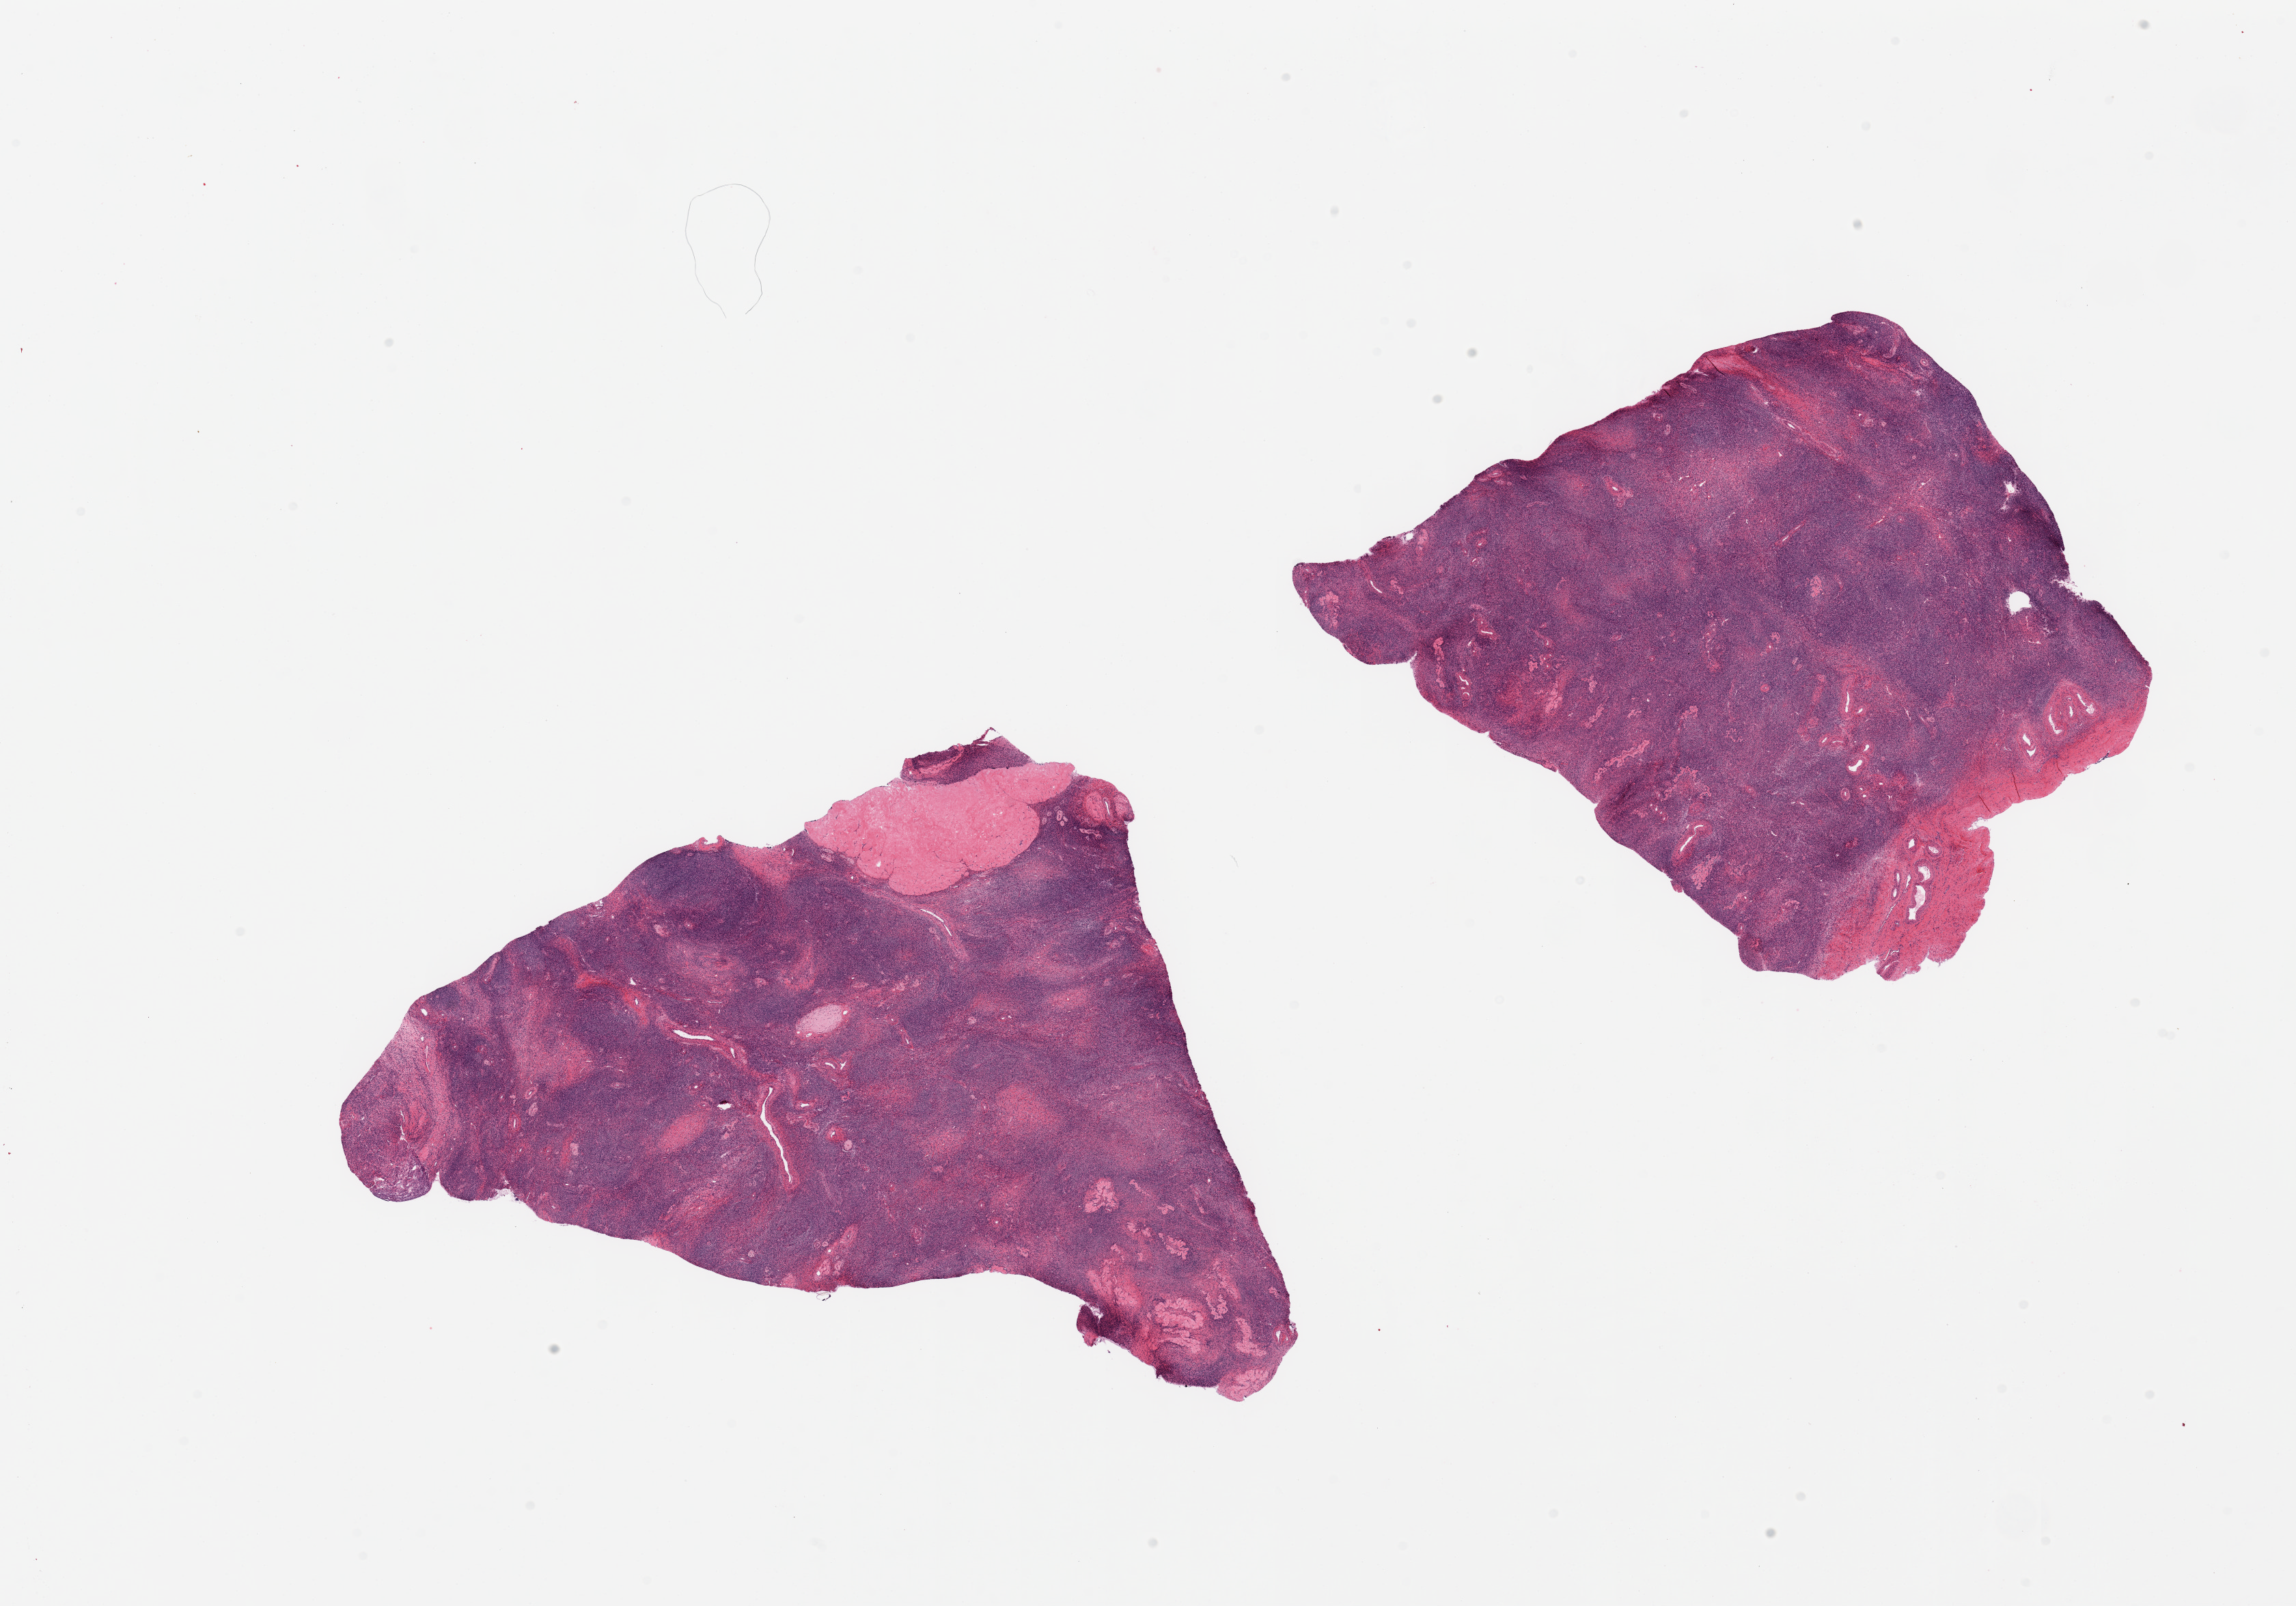
Whole-slide image, hematoxylin and eosin (H&E) stain, a low-resolution overview of the entire scanned area, about 26.6 x 18.6 mm, PAXgene-fixed, paraffin-embedded tissue, section of ovary (target tissue), tissue donor sample. Female donor.
Reviewer comment on this tissue sample: 2 pieces, corpora albicantia/fibrosa.